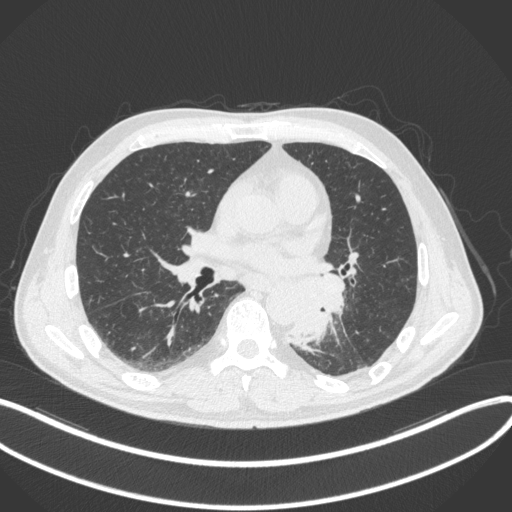
Chest CT, one axial slice; position 166 of 328 along the scan axis; reconstruction kernel B31f; 120 kVp; lung window (W 1500 / L -600 HU); 1 mm slice thickness; 512 × 512 image matrix, field of view 400 × 400 mm. Patient: male, 59 years. Case-level facts recorded for this patient, not image findings: clinical TNM (as recorded): T2a N2 M0.
Structures marked on this image (rectangle marked by the reading radiologist):
- lung tumour (recorded histology: squamous cell carcinoma): box from (x=292, y=274) to (x=346, y=344) px